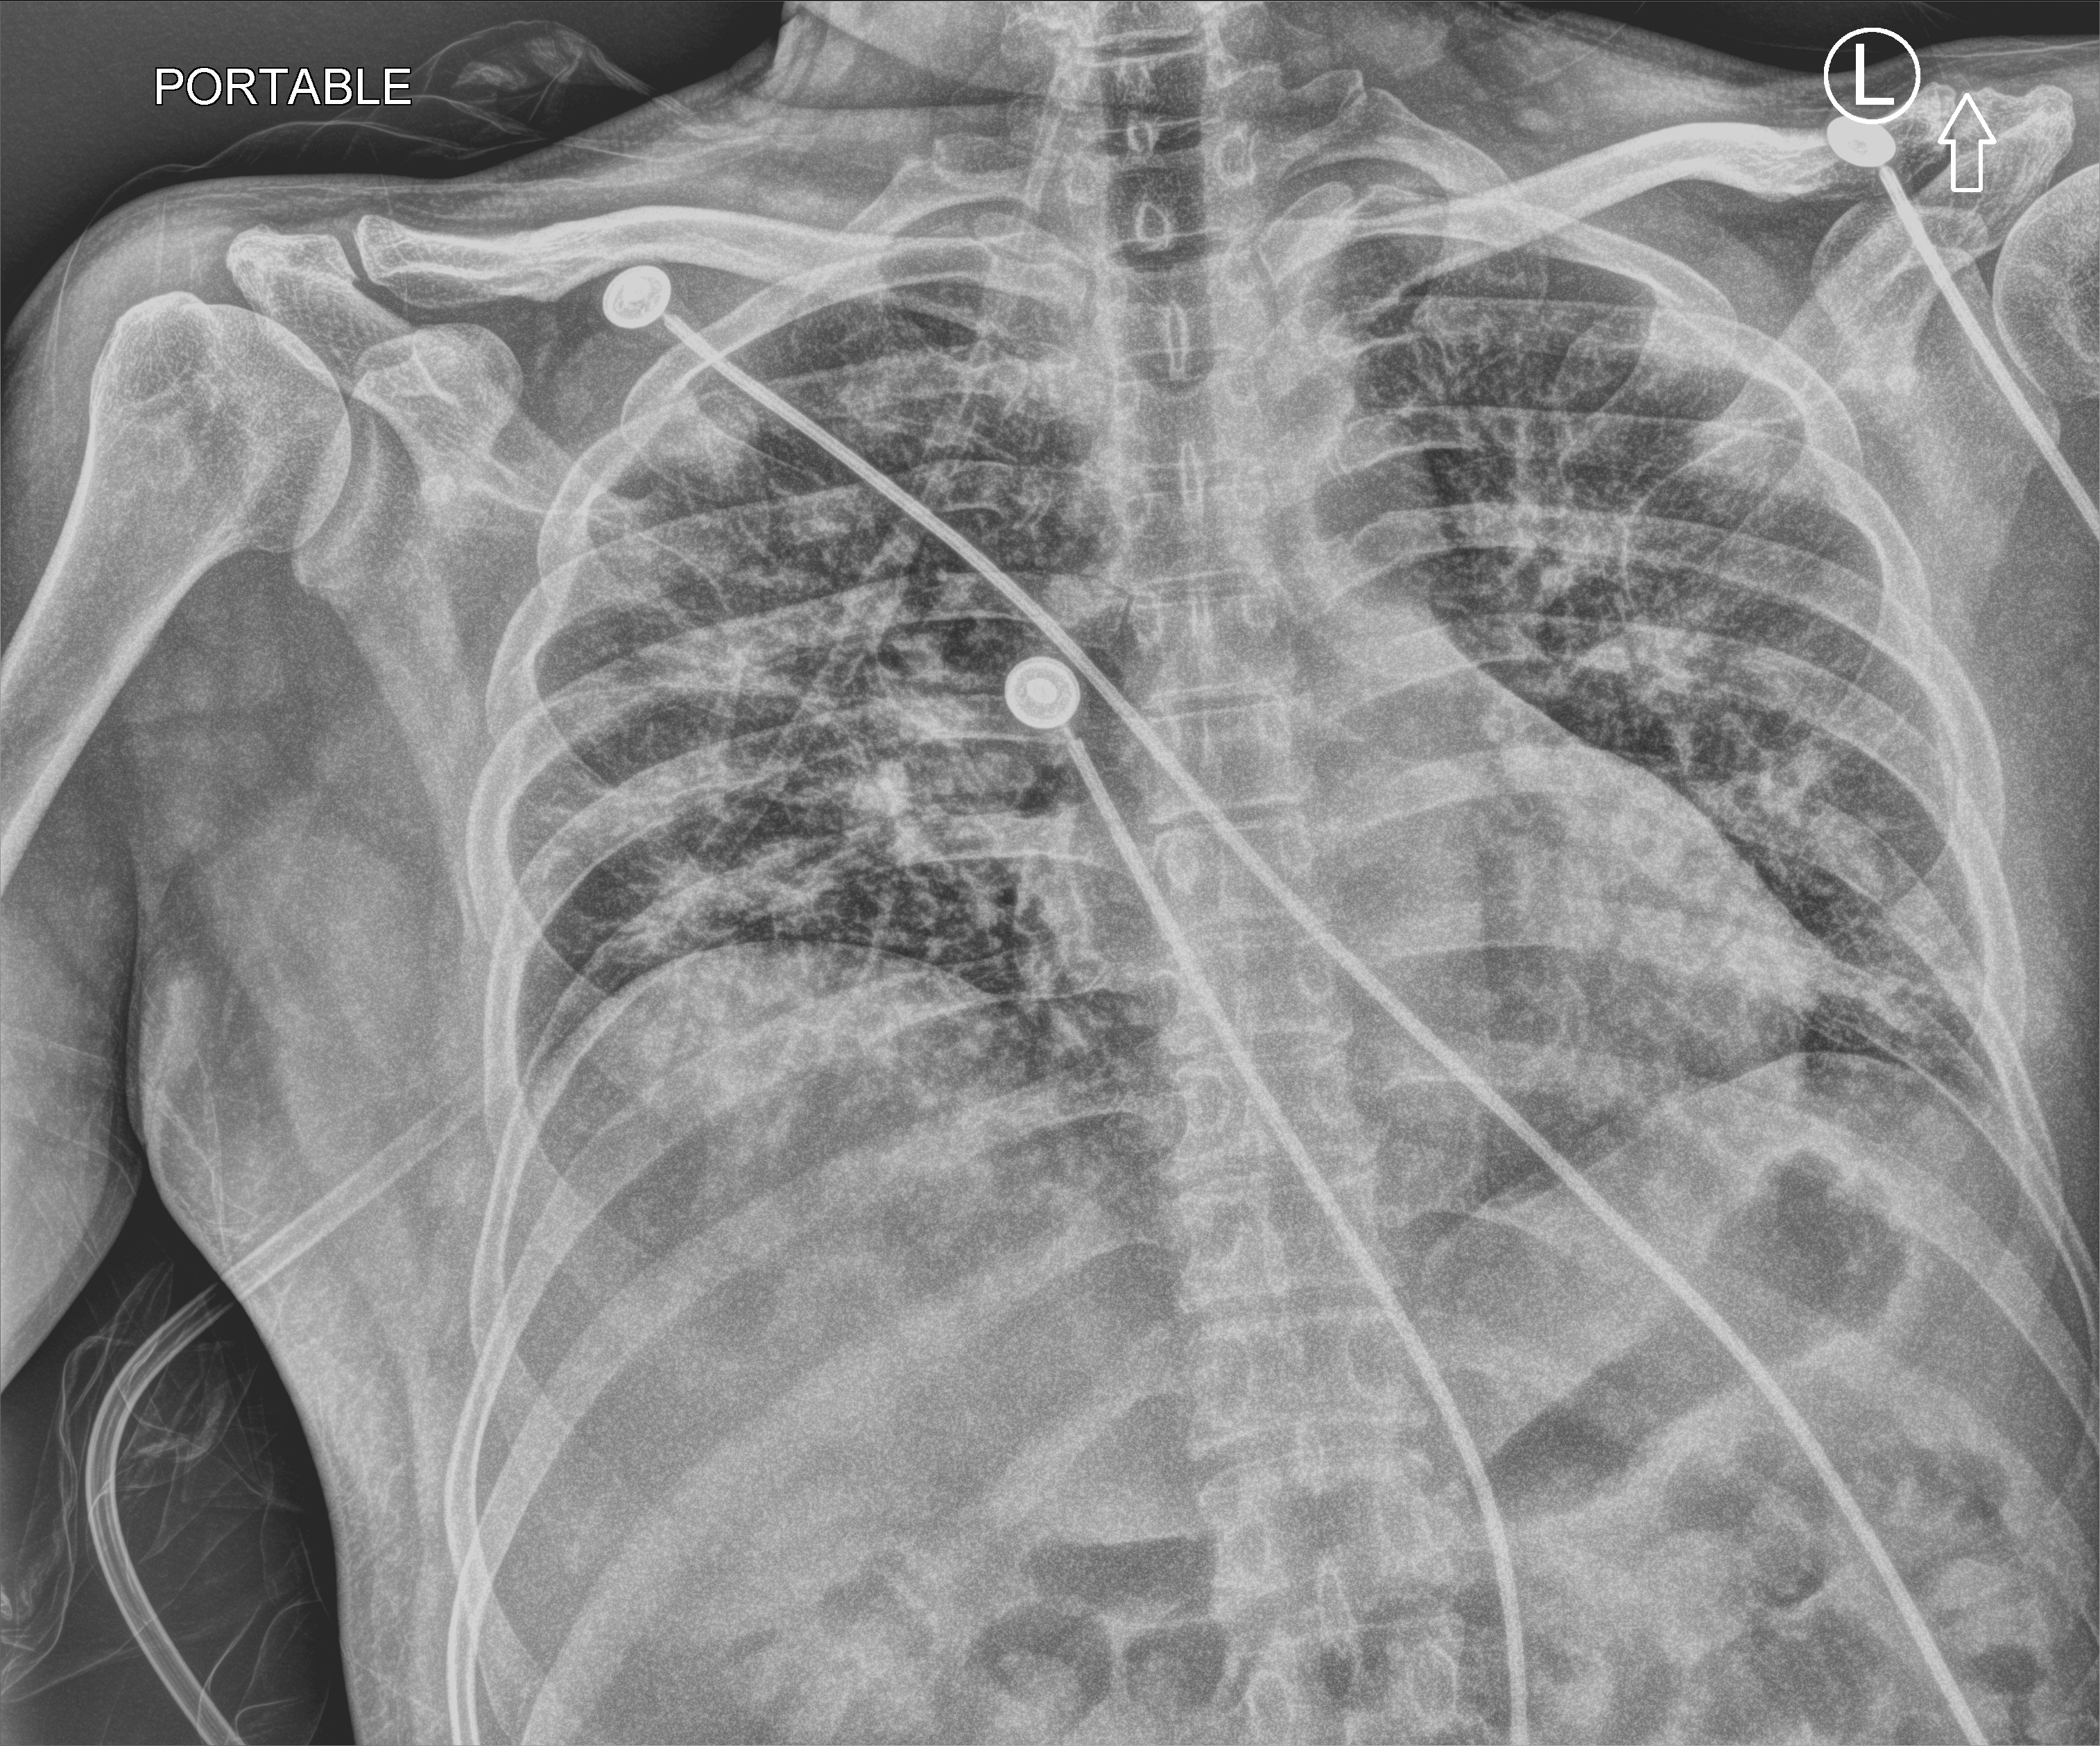
Chest X-ray (portable), anteroposterior (AP) projection. Patient hospitalised with COVID-19; male, aged 18–59 years.
Admission-level facts for this patient (not findings on this image; timing relative to this image not recorded): mechanically ventilated during this hospital stay: no.